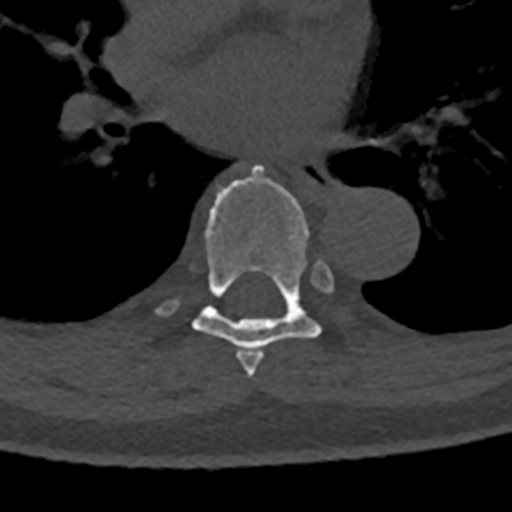
CT including the spine, one axial slice; position 764 of 797 along the scan axis; reconstruction kernel Br40s/3; bone window (W 1800 / L 400 HU); 512 × 512 image matrix. Male patient, age 74 years. Case-level facts recorded for this patient, not image findings: primary cancer: renal.
Annotated regions visible in this slice (semi-automatic segmentation, software-assisted and operator-edited):
- T6 vertebra: bounding box [x1, y1, x2, y2] px = [245, 352, 263, 377]
- T7 vertebra: [153, 165, 346, 367]